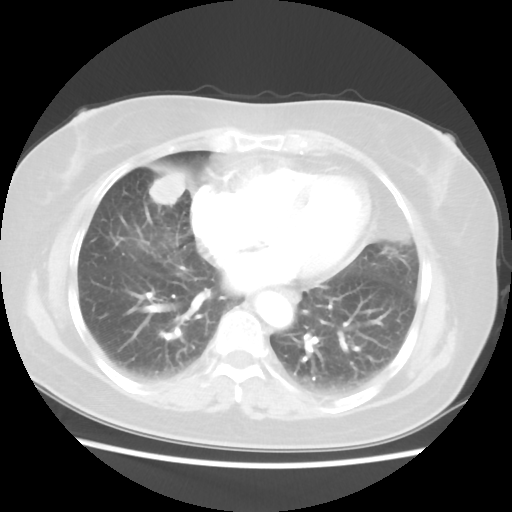
Chest CT, one axial slice. Position 19 of 48 along the scan axis. Reconstruction kernel STANDARD. Lung window (W 1500 / L -600 HU). 5 mm slice thickness. 512 × 512 image matrix, field of view 343 × 343 mm. Patient: female, 61 years. From the clinical record (not read from this slice): clinical TNM (as recorded): T1c N0 M0.
Annotated regions visible in this slice (bounding box drawn by a radiologist):
- lung tumour (recorded histology: adenocarcinoma): bounding box (x1, y1, x2, y2) in pixels: (146, 162, 187, 212)